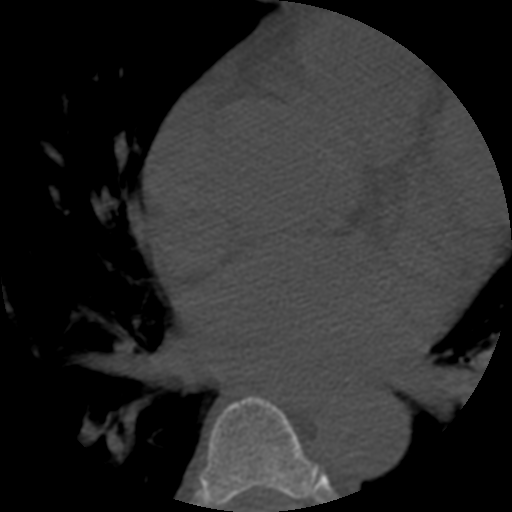
CT including the spine, one axial slice; slice 349 of 508 in the series (ordered by position); 120 kVp; bone window (W 1800 / L 400 HU); 1.25 mm slice thickness; 512 × 512 image matrix, field of view 160 × 160 mm. Patient age 57 years. Case-level facts recorded for this patient, not image findings: primary cancer: prostate.
Annotated regions visible in this slice (semi-automatic segmentation, software-assisted and operator-edited):
- T6 vertebra: bounding box [x1, y1, x2, y2] px = [200, 396, 320, 512]